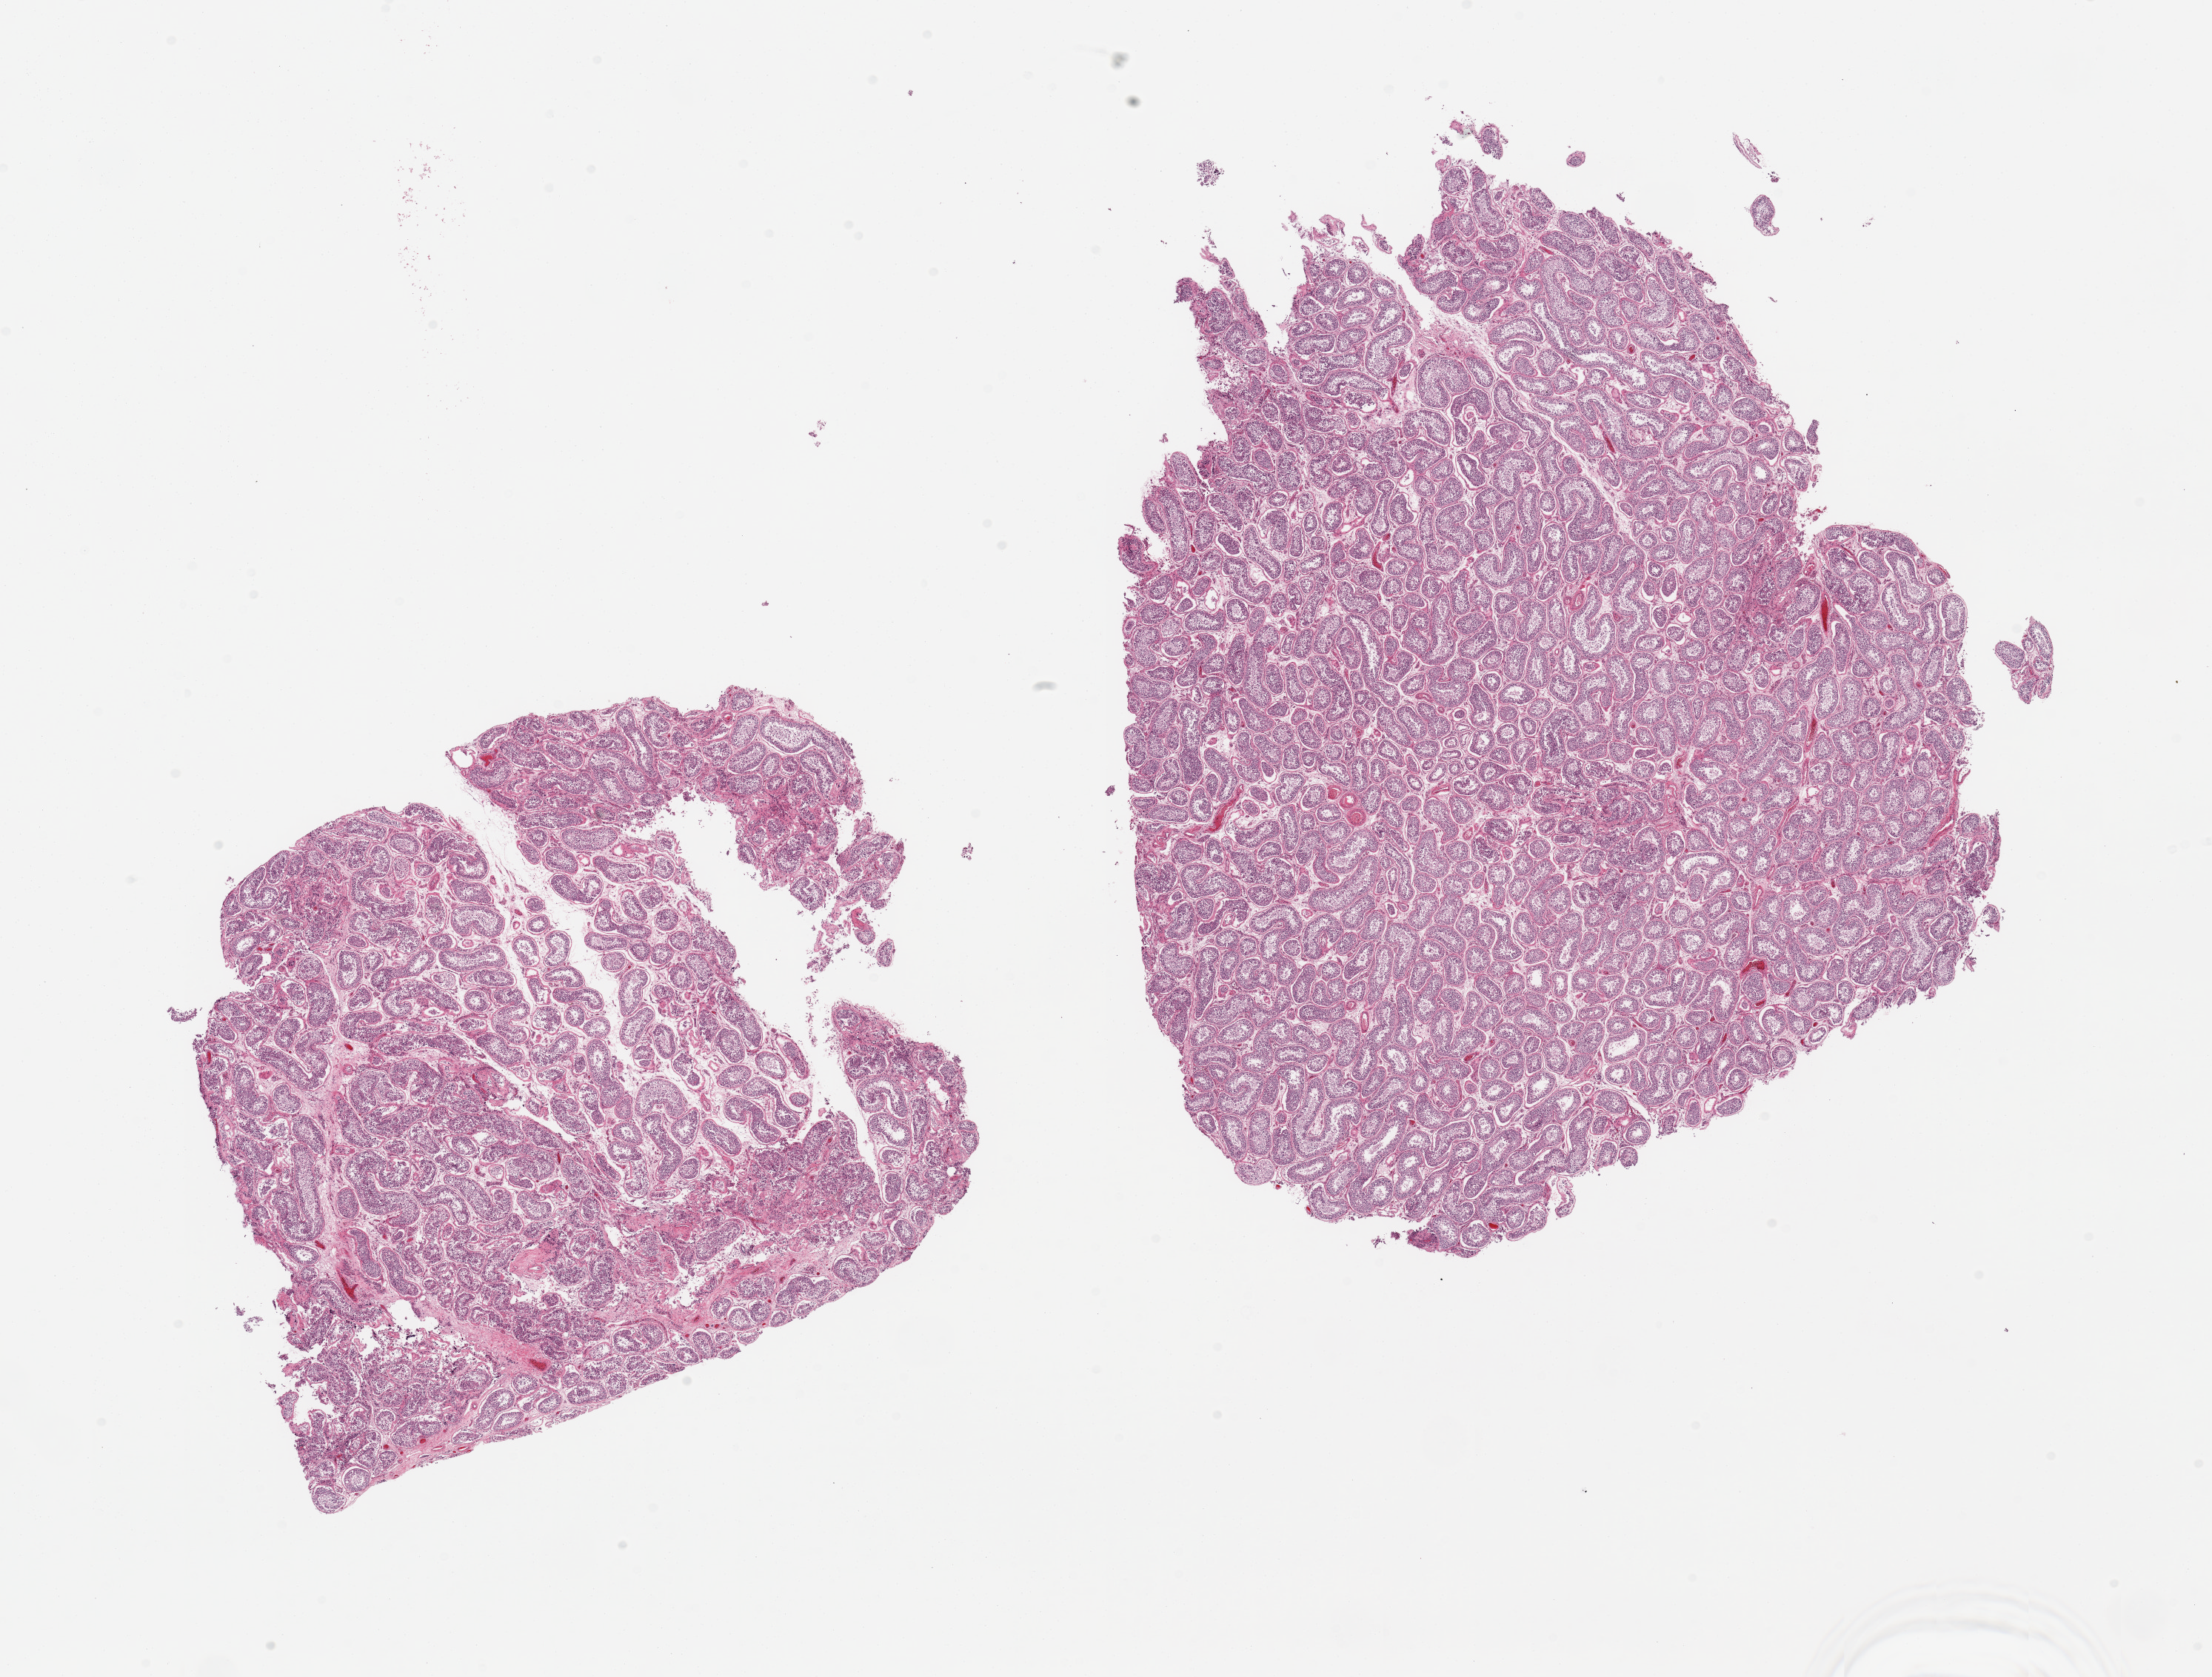
Whole-slide image, hematoxylin and eosin (H&E) stain — a low-resolution overview of the entire scanned area, about 23.6 x 17.9 mm. PAXgene-fixed paraffin-embedded (PFPE) section. Section of testis (target tissue). Donor tissue sample. Donor sex: male.
Reviewer comment on this tissue sample: 2 pieces, spermatogenesis is present.